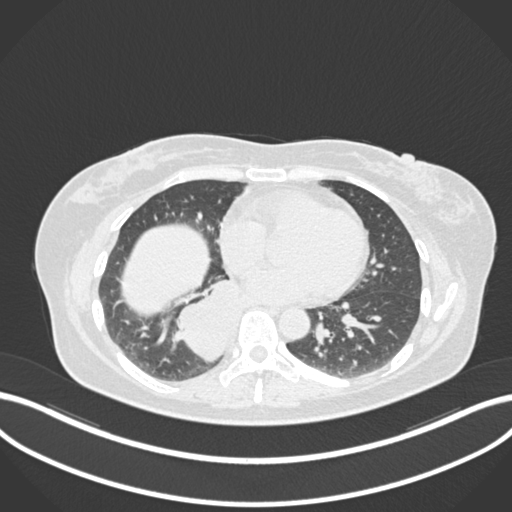
Chest CT, one axial slice; position 562 of 677 along the scan axis; 120 kVp; lung window (W 1500 / L -600 HU); 512 × 512 image matrix. Female patient, age 54 years. From the clinical record (not read from this slice): clinical TNM (as recorded): T4 N0 M0.
Structures marked on this image (rectangle marked by the reading radiologist):
- lung tumour (recorded histology: adenocarcinoma): bounding box <168,280,242,370> (left, top, right, bottom; pixels)